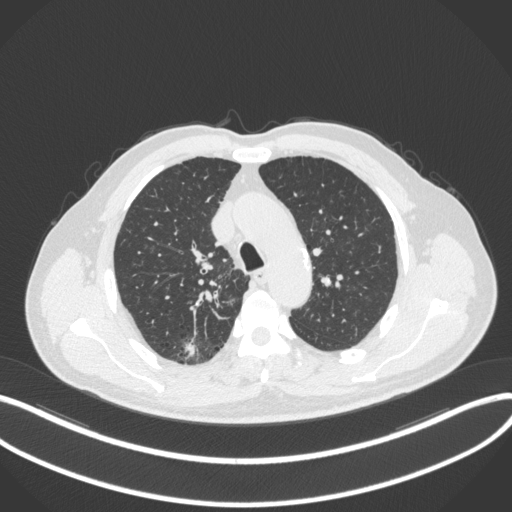
Chest CT, one axial slice. Position 274 of 366 along the scan axis. Reconstruction kernel B31f. Lung window (W 1500 / L -600 HU). 1 mm slice thickness. 512 × 512 image matrix, field of view 400 × 400 mm. Male patient, age 69 years. From the clinical record (not read from this slice): clinical TNM (as recorded): T1b N0 M0; histopathological grade: G2-3.
Annotated regions visible in this slice (rectangle marked by the reading radiologist):
- lung tumour (recorded histology: adenocarcinoma): bounding box [x1, y1, x2, y2] px = [179, 337, 198, 360]